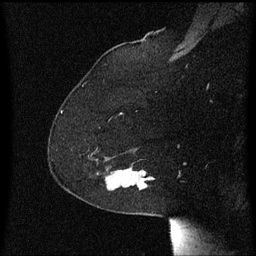
Breast MRI (dynamic contrast-enhanced), one sagittal slice; slice 44 of 60 in the series (ordered by position); dynamic contrast-enhanced series, image 2 of 3 at this slice position (ordered by acquisition); 1.5 T; TE 4.2 ms, TR 8.4 ms; 2 mm slice thickness; 256 × 256 image matrix, field of view 200 × 200 mm. Patient: female, 59 years.
Annotated regions visible in this slice (semi-automatic segmentation, software-assisted and operator-edited):
- analysis volume of interest (the breast-tissue region the enhancement analysis was run in; not a lesion): bounding box (x1, y1, x2, y2) in pixels: (98, 168, 153, 191)
- tumour enhancement mask (voxels above the 70 % enhancement threshold inside the analysis volume of interest): (140, 172, 153, 181)